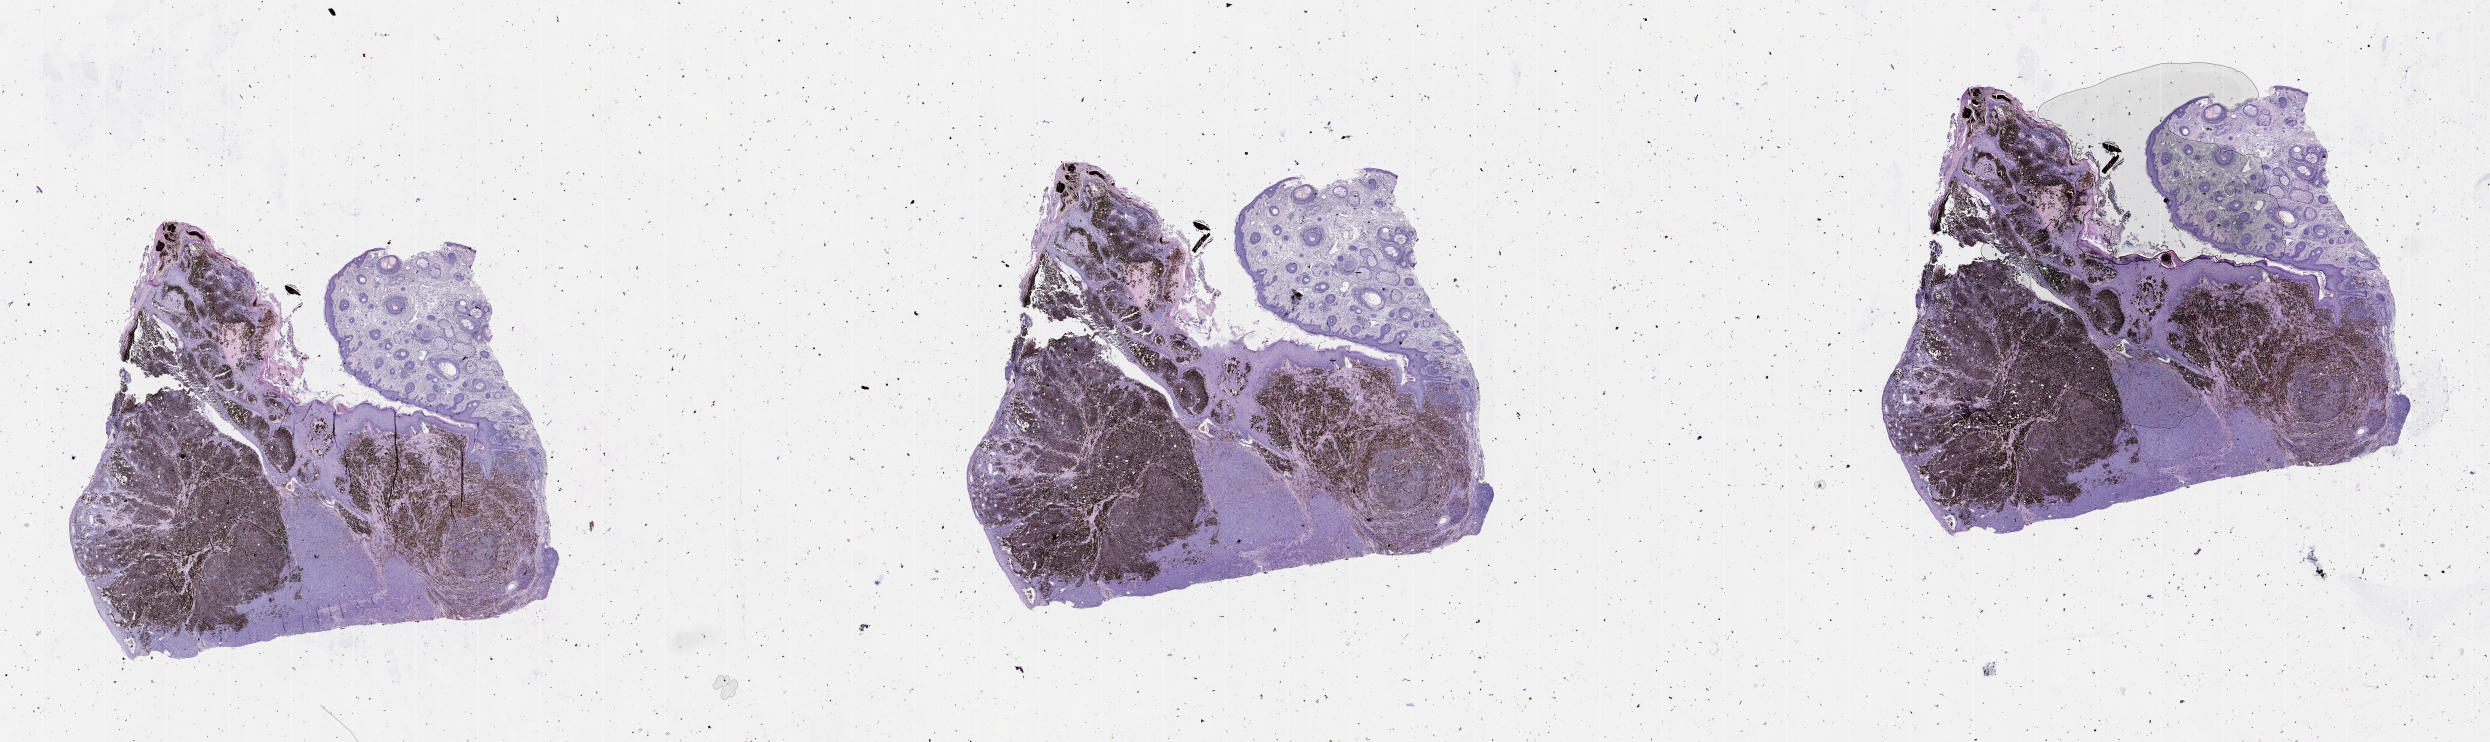
Digitized H&E-stained tissue section (whole slide) — low-resolution overview of the scanned area, about 40.1 x 11.9 mm. Melanoma tumour tissue; sampled site not recorded. 83-year-old male patient.
Primary tumour site (as recorded): head & neck. AJCC pathologic stage: IIC. Histologic diagnosis: Malignant melanoma, NOS.